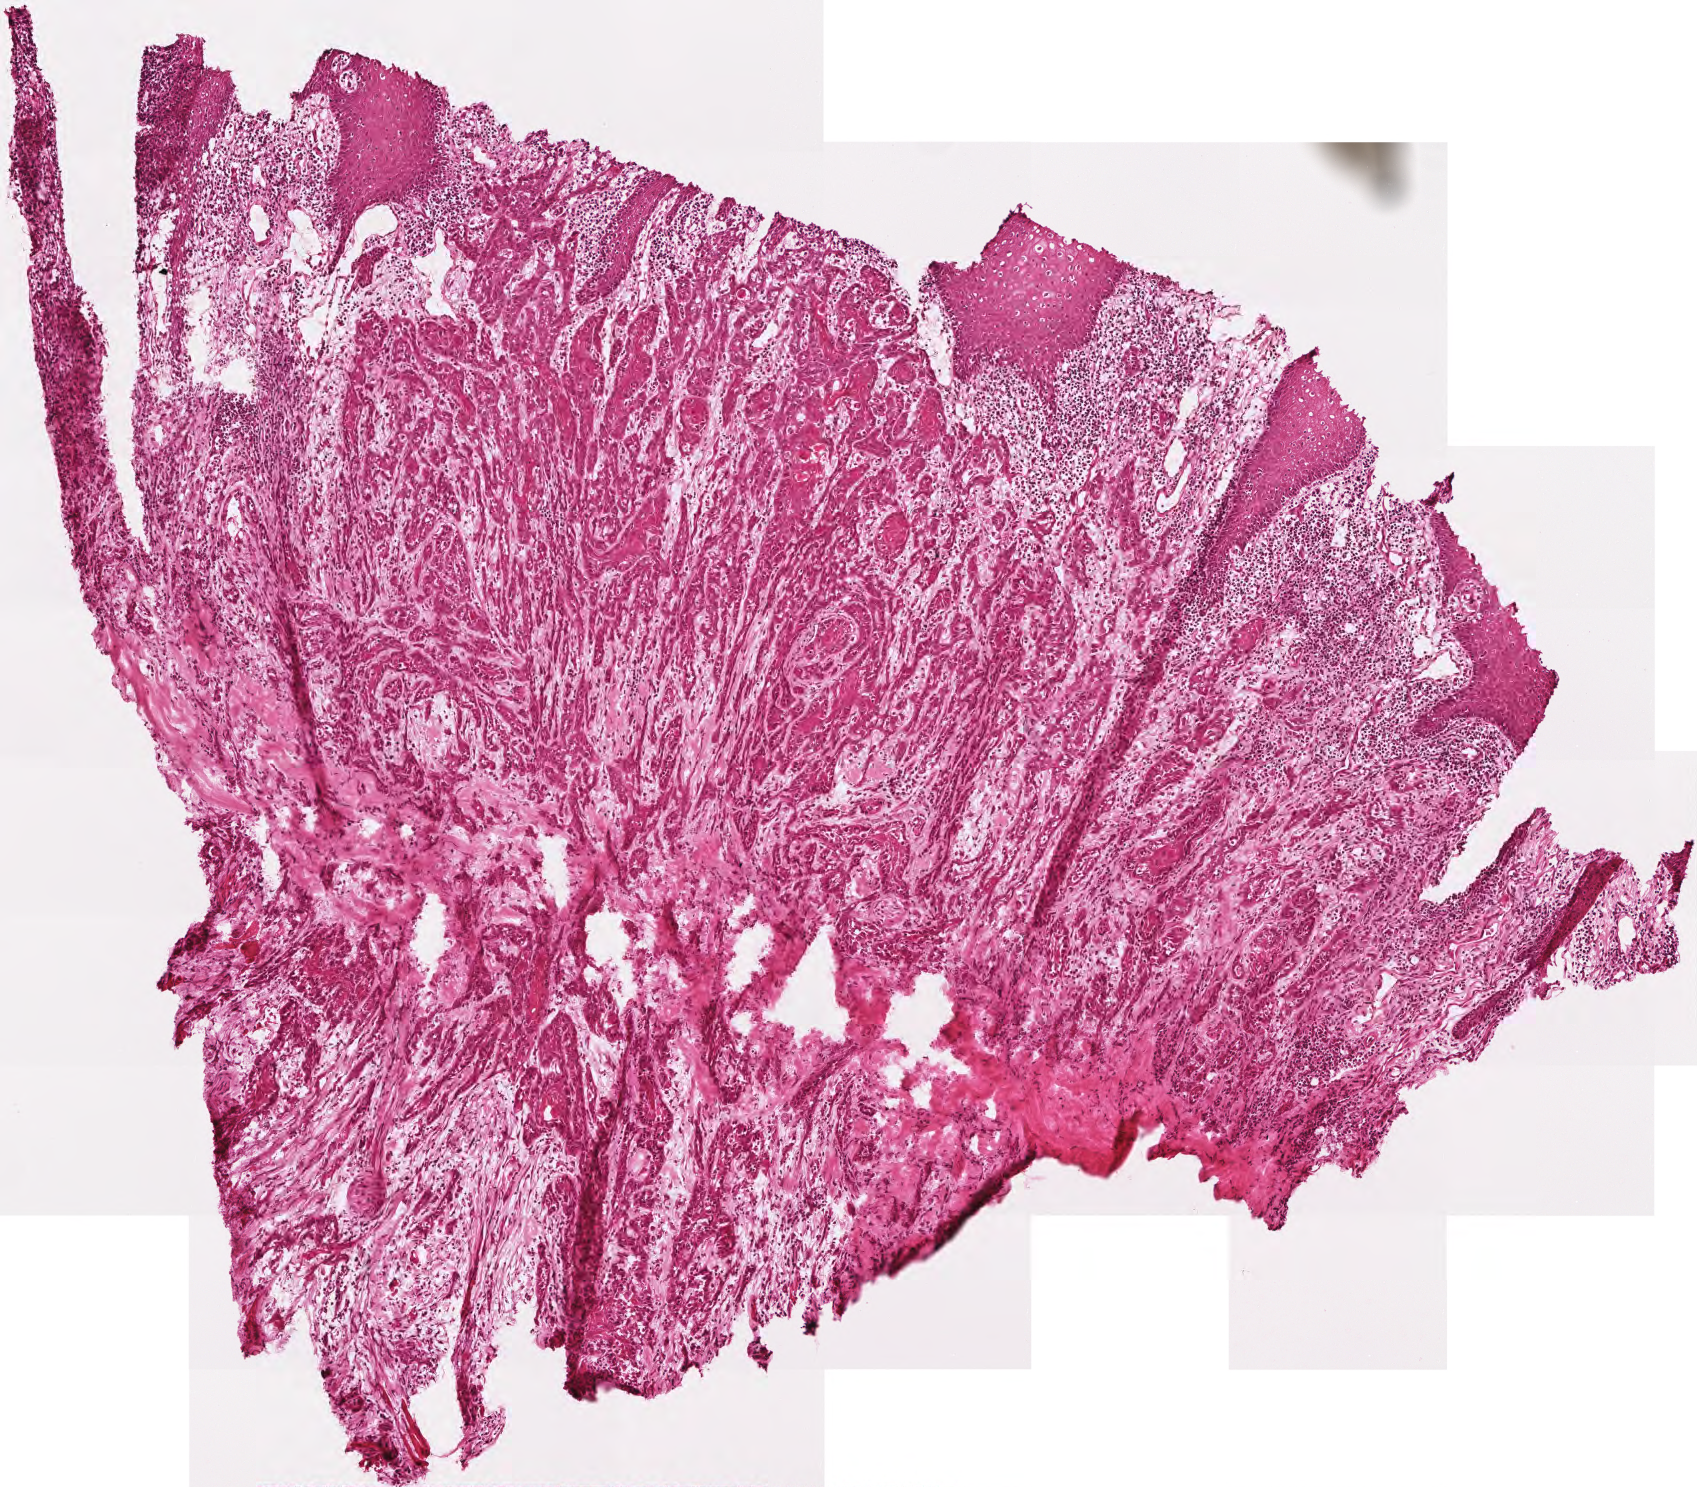
Whole-slide histology image, Hematoxylin and eosin (H&E) stained, whole scanned area (about 3.4 x 3.0 mm) shown as a low-resolution overview. Frozen section from the top of the tissue portion. Head and neck, primary tumour sample. Male patient; age at initial diagnosis 58 years. Histologic grade: G3 (poorly differentiated). Pathologist review of this section (percent, as recorded): tumour cells 68%, tumour nuclei 70%, normal cells 7%, stromal cells 25%, necrosis 0%.
Lymph nodes positive (case pathology): 3 of 29 examined. Histologic diagnosis: Squamous cell carcinoma, NOS (overlapping lesion of lip, oral cavity and pharynx). TNM: T4a N2c M0. AJCC pathologic stage: IVA (6th edition).